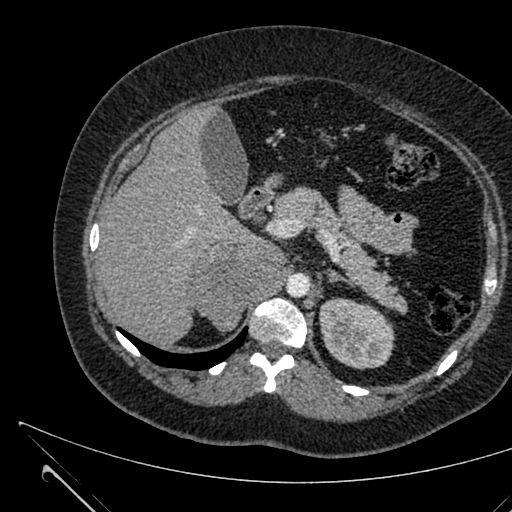
Contrast-enhanced abdominal CT, one axial slice; position 431 of 731 along the scan axis; intravenous contrast given; soft-tissue window (W 400 / L 40 HU); 1 mm slice thickness; 512 × 512 image matrix, field of view 376 × 376 mm. Female patient, age 36 years. From the clinical record (not read from this slice): diagnosis: adrenocortical carcinoma; tumour side: right adrenal; tumour size at pathology: 10 cm; Ki-67 index: 20 %; stage (as recorded): 4.
Annotated regions visible in this slice (semi-automatically segmented with operator editing):
- mass: box from (x=192, y=244) to (x=288, y=332) px